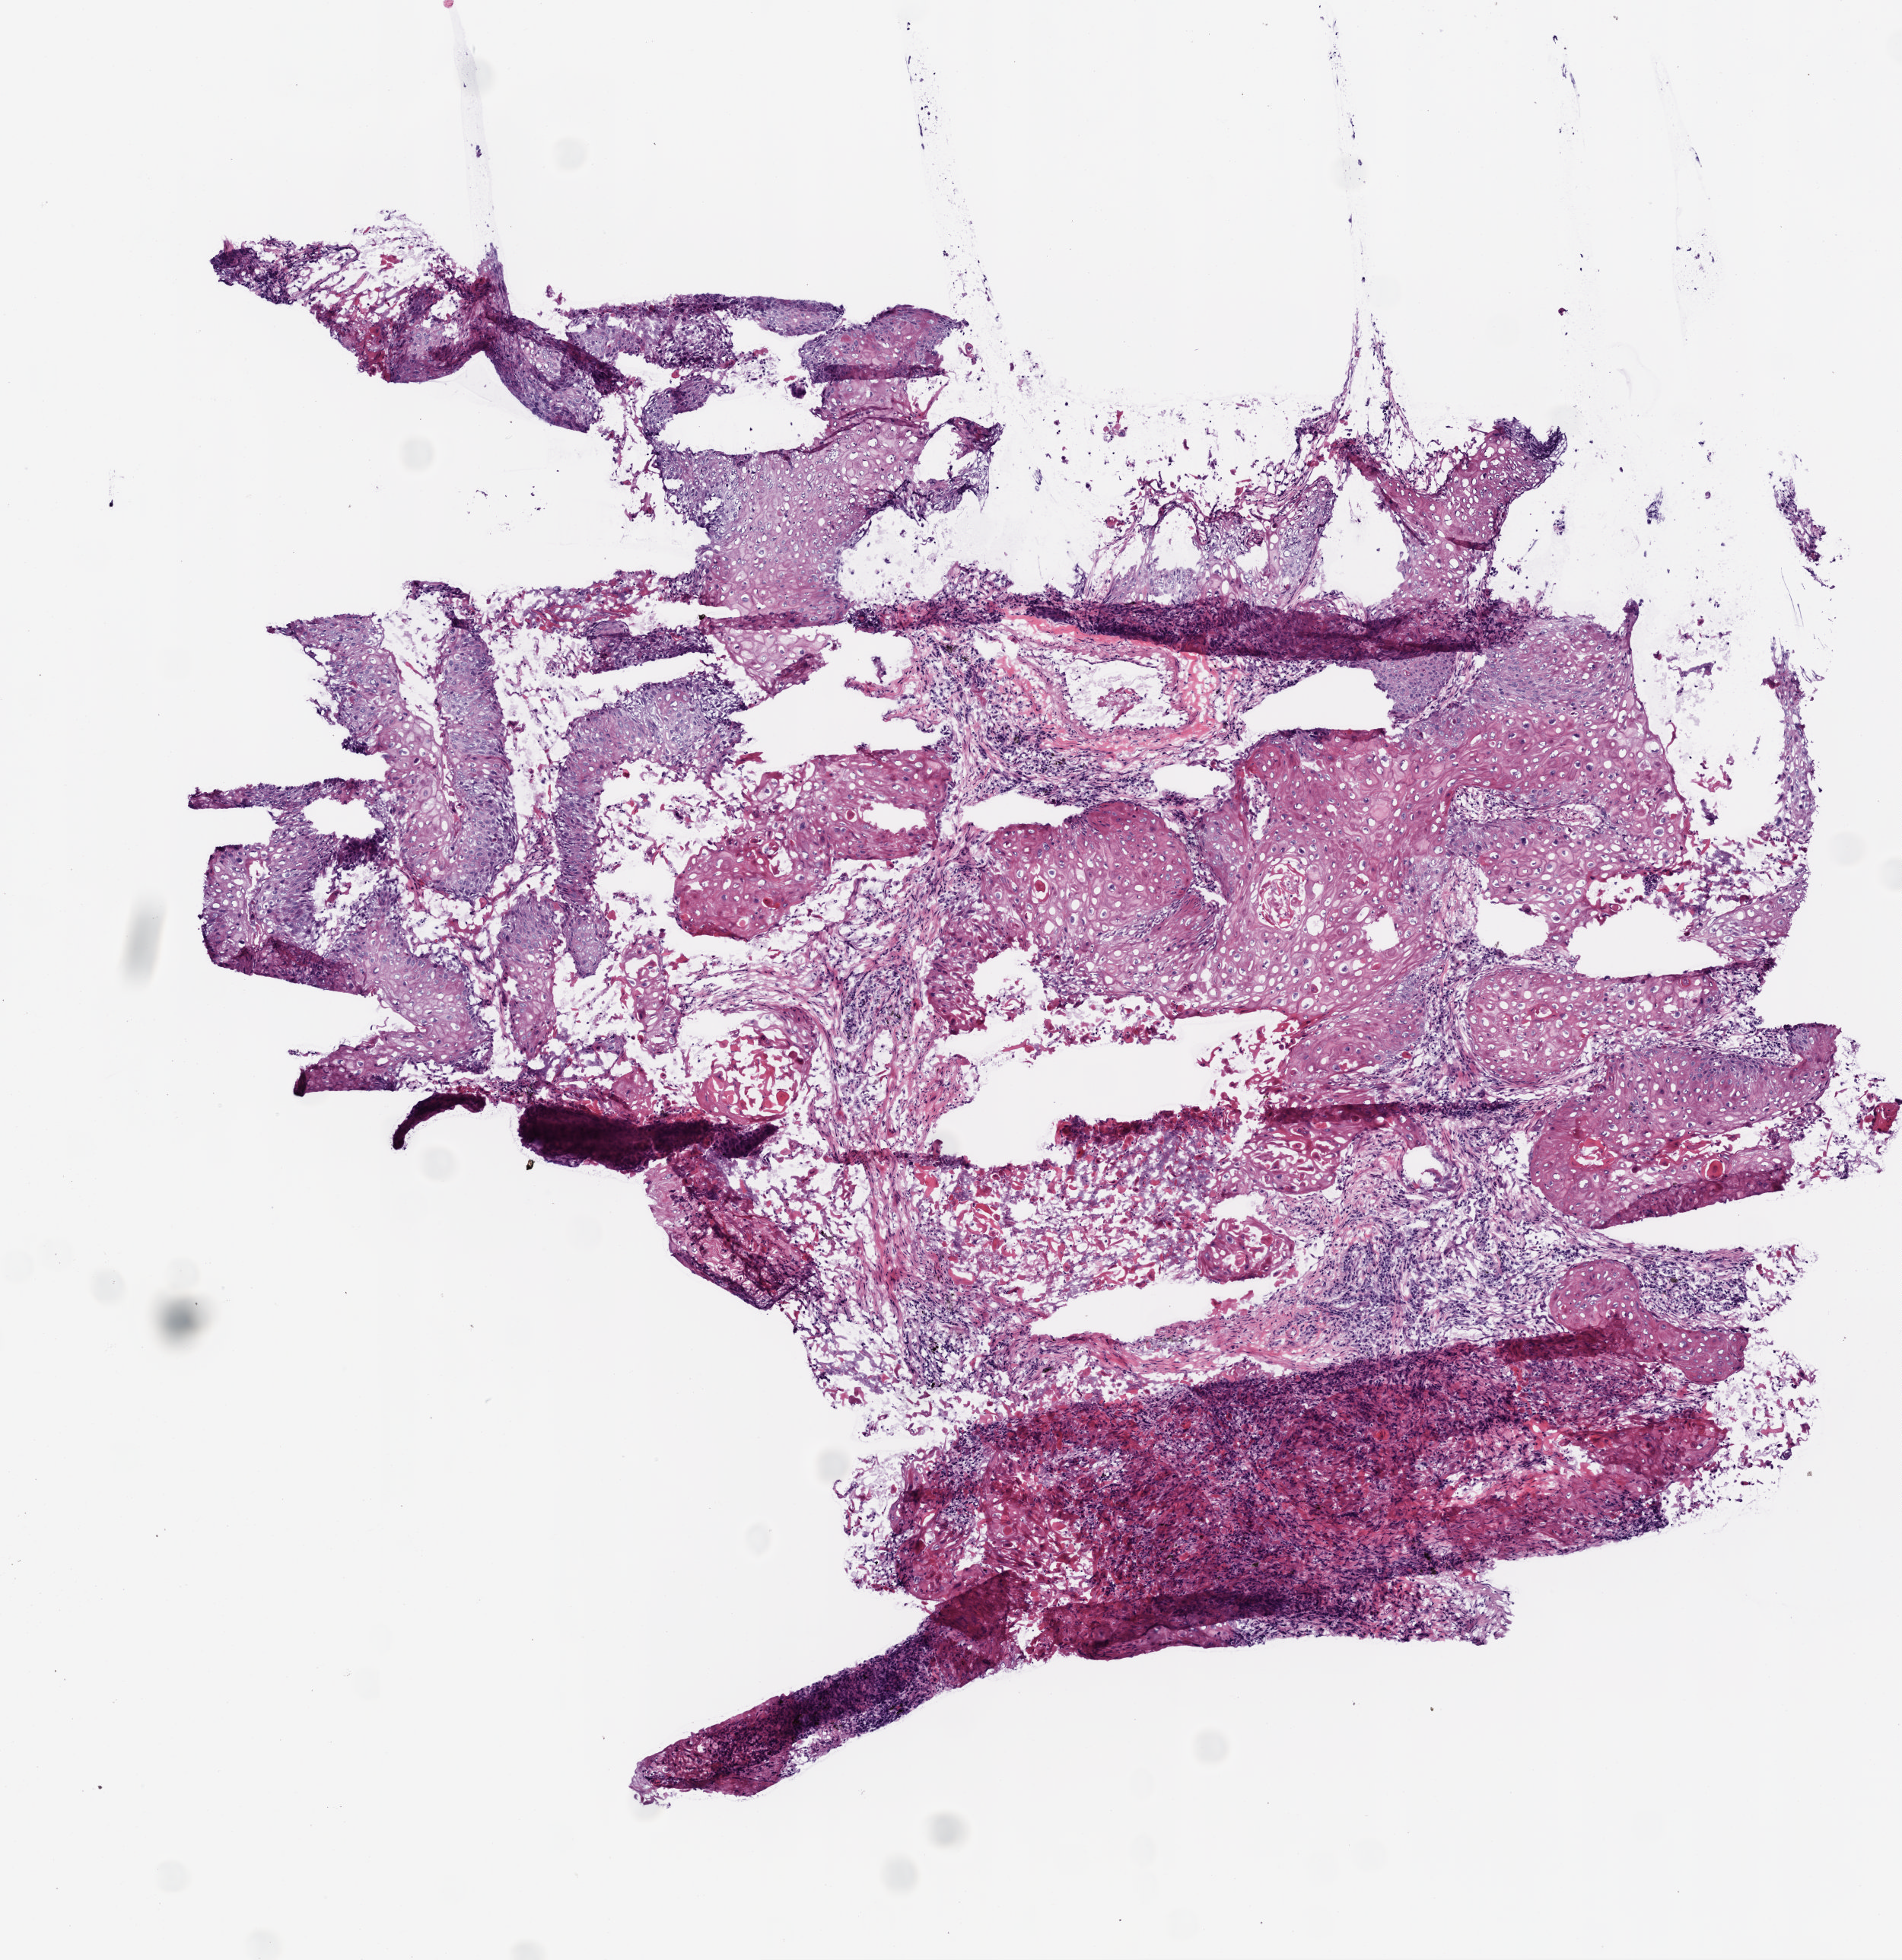
Whole-slide histology image, H&E-stained, whole scanned area (about 5.0 x 5.2 mm, acquisition: 20x scan) shown as a low-resolution overview, frozen section from the top of the tissue portion, primary tumour sample from the lung. Male patient; age at initial diagnosis 67 years. Slide review estimates, as recorded: tumour cells 80%, tumour nuclei 80%, normal cells 0%, stromal cells 19%, necrosis 1%. Inflammatory infiltration, as recorded: lymphocyte infiltration 10%.
Pathologic diagnosis: Squamous cell carcinoma, NOS (upper lobe, lung). AJCC pathologic stage: IA.